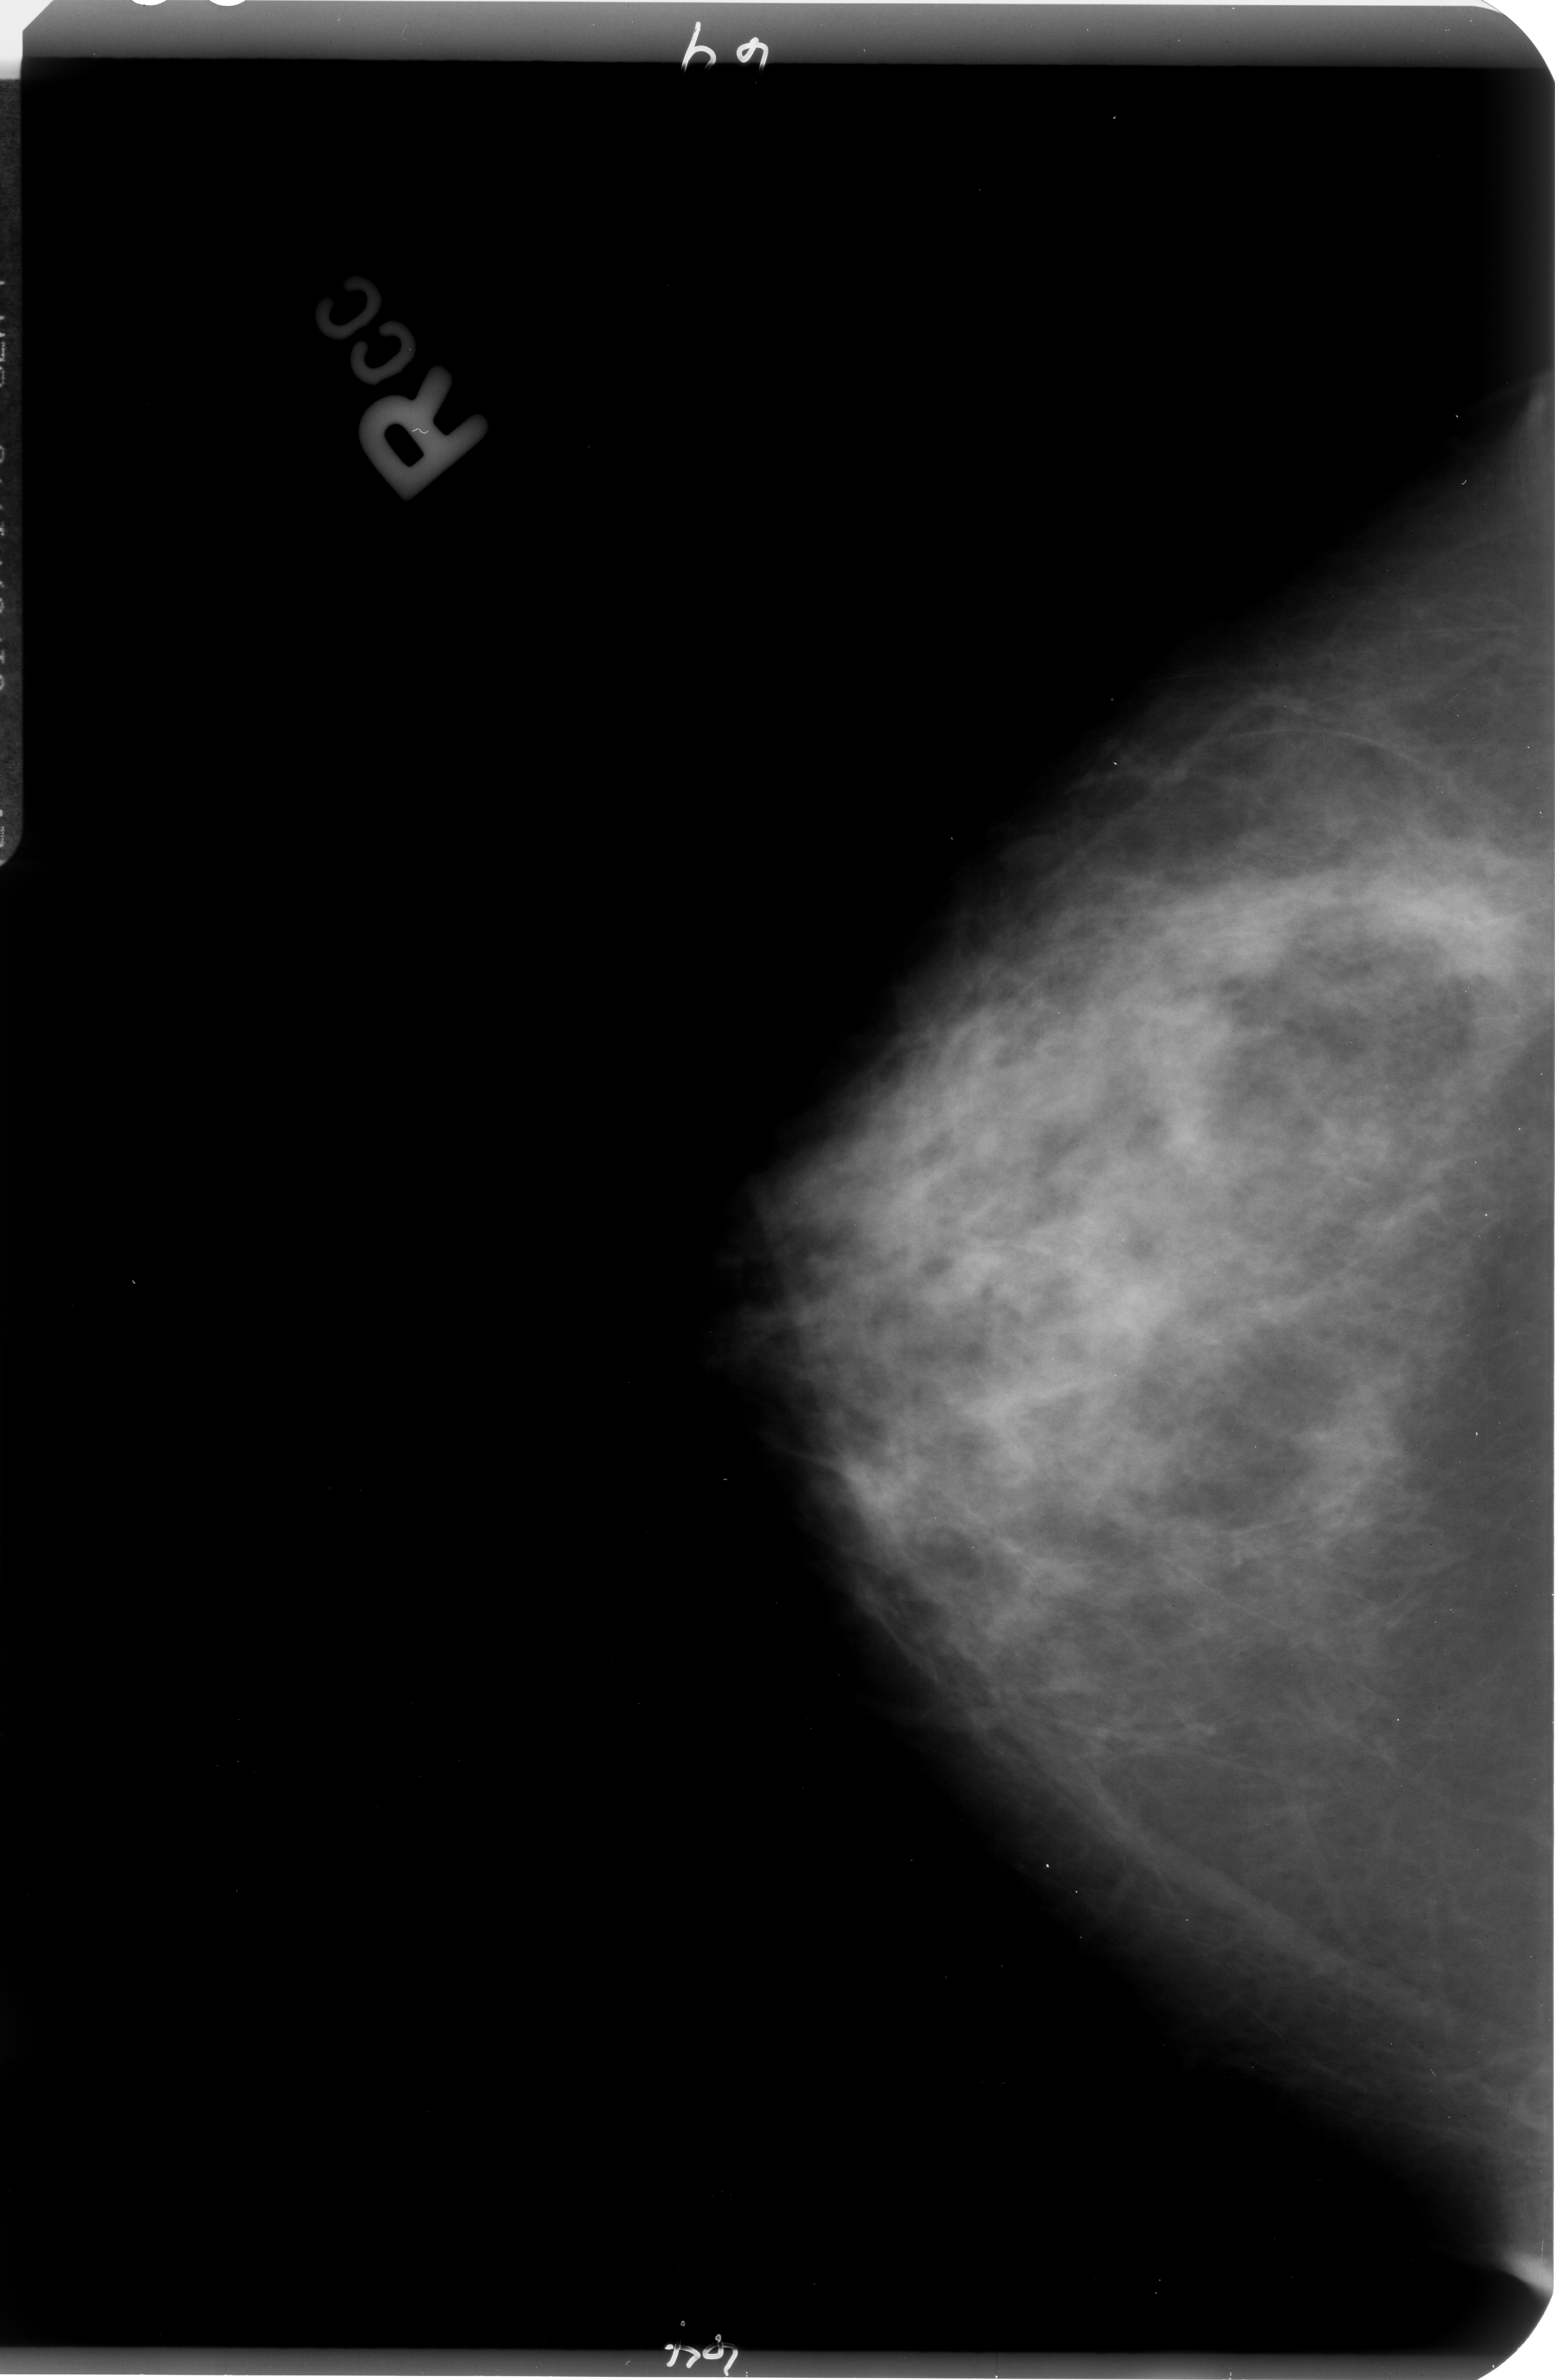
Digitized screen-film mammogram; right breast; craniocaudal (CC) view; BI-RADS breast density category 3 (scale 1–4); 1555 × 2380 image matrix.
Expert-marked regions of interest on this image (one box per marked abnormality):
- mass, shape architectural distortion, margins ill defined; BI-RADS assessment category 4; subtlety rating 2 on a 1 (subtle) to 5 (obvious) scale; pathology (as recorded): malignant: bounding box (x1, y1, x2, y2) in pixels: (1364, 864, 1517, 992)